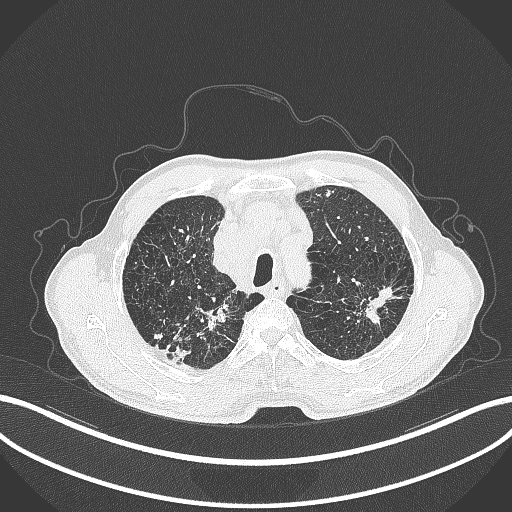
Chest CT, one axial slice; slice 363 of 463 in the series (ordered by position); reconstruction kernel B70f; lung window (W 1500 / L -600 HU); 1 mm slice thickness; 512 × 512 image matrix, field of view 400 × 400 mm. Male patient, age 74 years. Case-level facts recorded for this patient, not image findings: clinical TNM (as recorded): T2a N1 M0.
Annotated regions visible in this slice (bounding box drawn by a radiologist):
- lung tumour (recorded histology: adenocarcinoma): bounding box <368,282,402,334> (left, top, right, bottom; pixels)